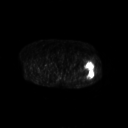
FDG PET of an extremity soft-tissue mass (from a PET/CT study), one axial slice. Slice 252 of 267 in the series (ordered by position). 3.27 mm slice thickness. 128 × 128 image matrix, field of view 700 × 700 mm. Patient: female, 62 years. From the clinical record (not read from this slice): histological type: undifferentiated – high grade; grade: high; site of the primary tumour: left thigh.
Outlined on this slice (expert contour drawn on MRI and transferred to this co-registered scan by the dataset authors):
- gross tumour volume including surrounding oedema: box from (x=84, y=62) to (x=95, y=79) px
- gross tumour volume (mass): (x=85, y=62)–(x=95, y=78)